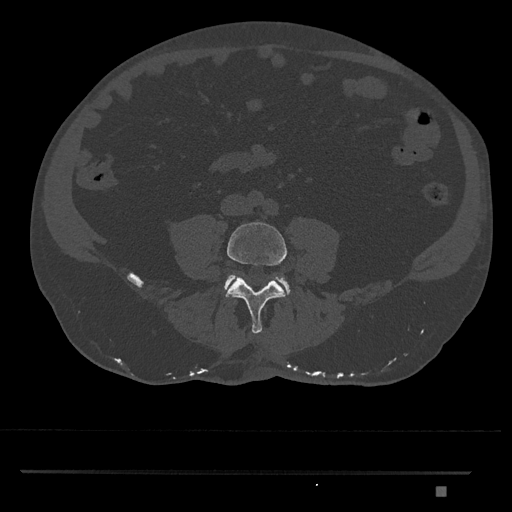
CT including the spine, one axial slice; slice 602 of 1134 in the series (ordered by position); reconstruction kernel Br40s/3; bone window (W 1800 / L 400 HU); 0.5 mm slice thickness; 512 × 512 image matrix, field of view 429 × 429 mm. Patient: male, 65 years. Case-level facts recorded for this patient, not image findings: primary cancer: prostate.
Structures marked on this image (semi-automatic segmentation, software-assisted and operator-edited):
- L4 vertebra: bounding box (x1, y1, x2, y2) in pixels: (226, 222, 287, 334)
- L5 vertebra: (224, 275, 290, 294)